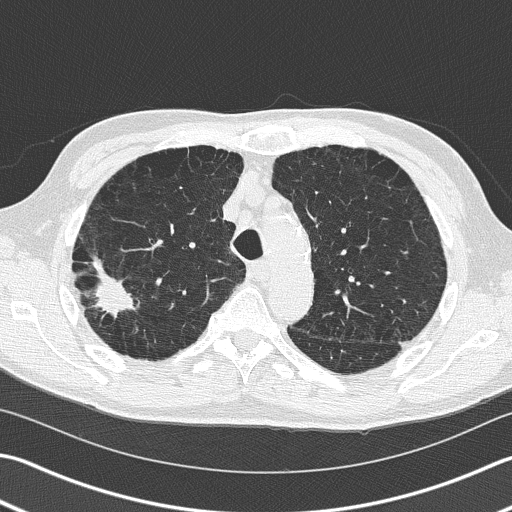
Chest CT (low-dose screening protocol), one axial image. Baseline annual screen. Lung window (W 1500 / L -600 HU). Slice 48 of 163 in the series. 512 × 512 image matrix. Male participant, aged 66 years at enrolment. Current smoker at enrolment.
• Lesion marked by an expert reader, bounding box [x1, y1, x2, y2] px = [70, 251, 139, 338].
• Reader record for this screening exam (exam-level; its link to the box is not recorded): non-calcified nodule or mass ≥4 mm, right upper lobe, 39 × 23 mm, spiculated (stellate) margins, soft tissue attenuation.
• Lung cancer was diagnosed 36 days after this screen: squamous cell carcinoma, NOS, right upper lobe, poorly differentiated (G3), stage IB (AJCC 6th edition), 23 mm at pathology.